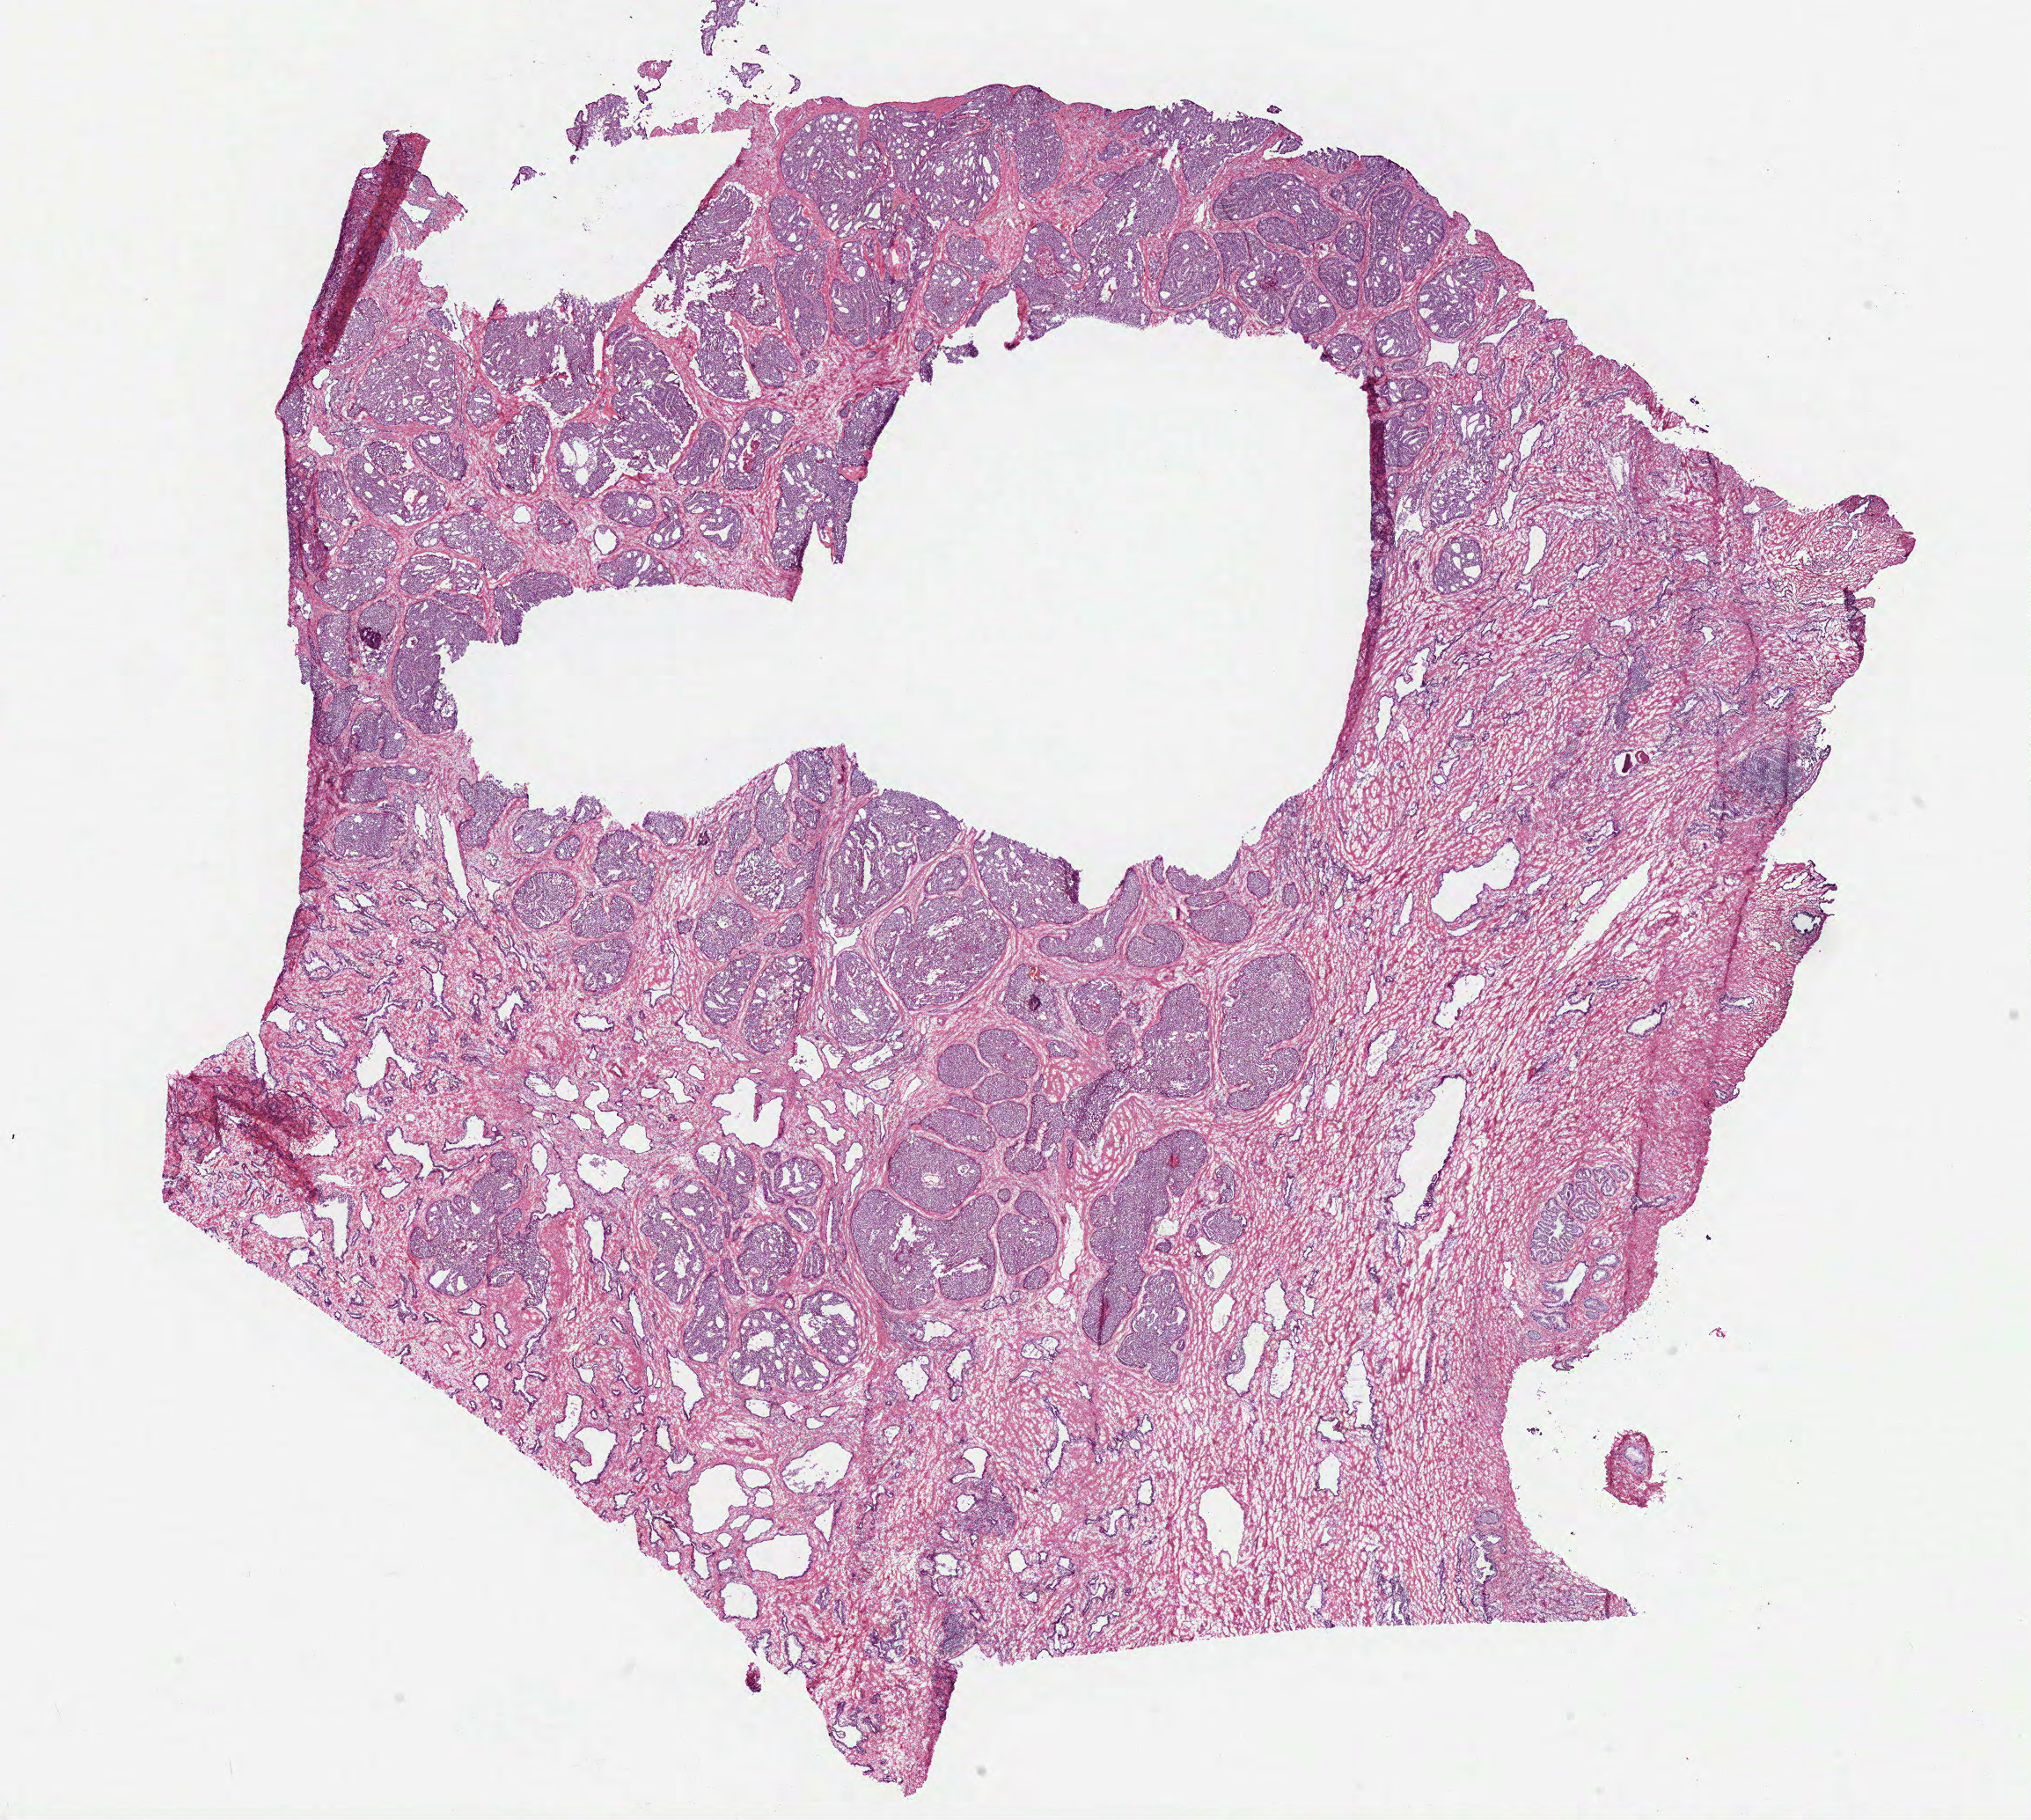
Digitized H&E-stained tissue section (whole slide), low-resolution overview of the scanned area, about 18.6 x 16.7 mm, frozen section from the bottom of the tissue portion, prostate, primary tumour sample. Male patient; age at initial diagnosis 71 years. Gleason score: 8 (4+4). Composition of this section per pathologist review: tumour cells 60%, tumour nuclei 70%, normal cells 10%, stromal cells 29%, necrosis 1%. Inflammatory infiltration, as recorded: lymphocyte infiltration 2%, monocyte infiltration 0%, neutrophil infiltration 0%.
Lymph nodes positive (case pathology): 0 of 17 examined. Diagnosis: Acinar cell carcinoma (prostate gland).